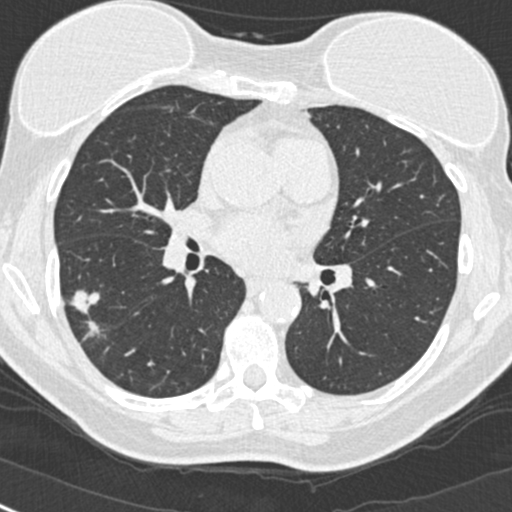
Low-dose screening chest CT, one axial slice; reconstruction kernel B30f; lung window (W 1500 / L -600 HU); 512 × 512 image matrix.
Structures marked on this image (outlined manually by an expert reader):
- lesion 1 (tumor, upper lobe of right lung): bounding box [x1, y1, x2, y2] px = [72, 290, 100, 337]